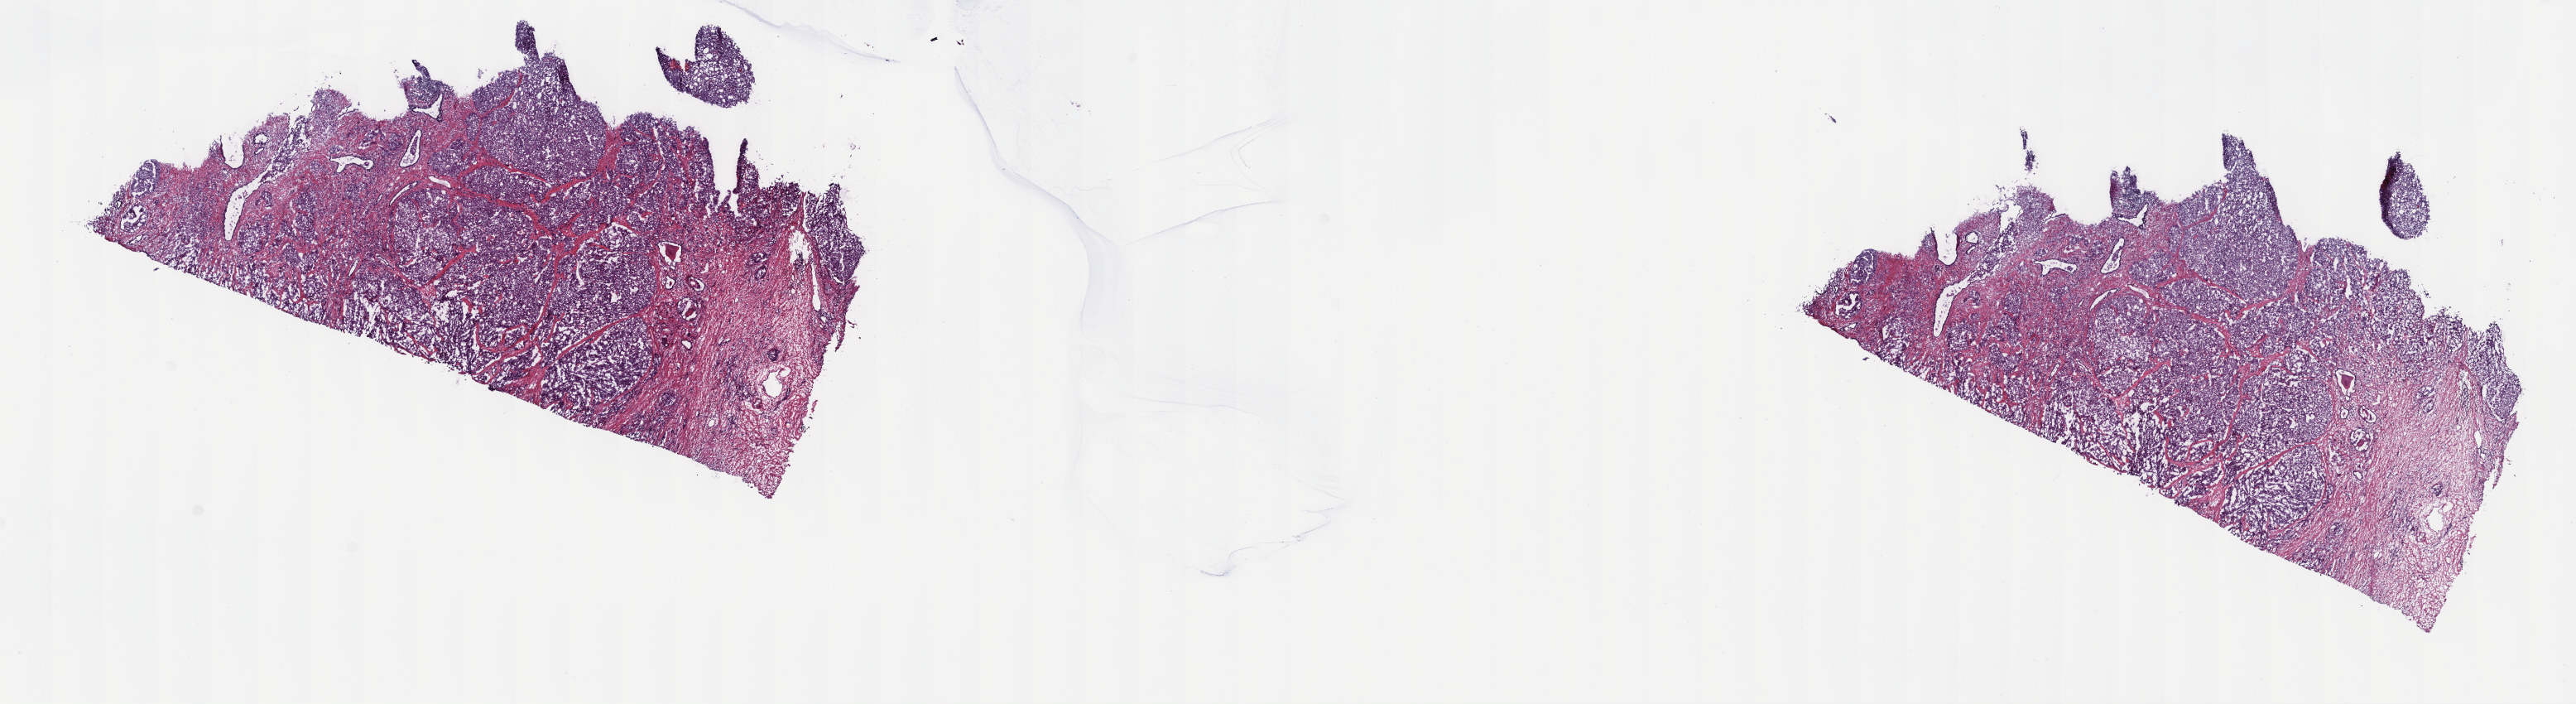
Digitized H&E-stained tissue section (whole slide), a low-resolution overview of the entire scanned area, about 25.2 x 6.9 mm (acquisition: 40x scan); frozen section from the top of the tissue portion; primary tumour sample from the prostate. Male patient; age at initial diagnosis 65 years. Gleason score: 9 (5+4). Pathologist review of this section (percent, as recorded): tumour cells 70%, tumour nuclei 70%, normal cells 0%, stromal cells 30%, necrosis 0%. Infiltration values recorded for this section: lymphocyte infiltration 40%, monocyte infiltration 20%, neutrophil infiltration 20%.
- diagnosis: Adenocarcinoma, NOS (prostate gland)